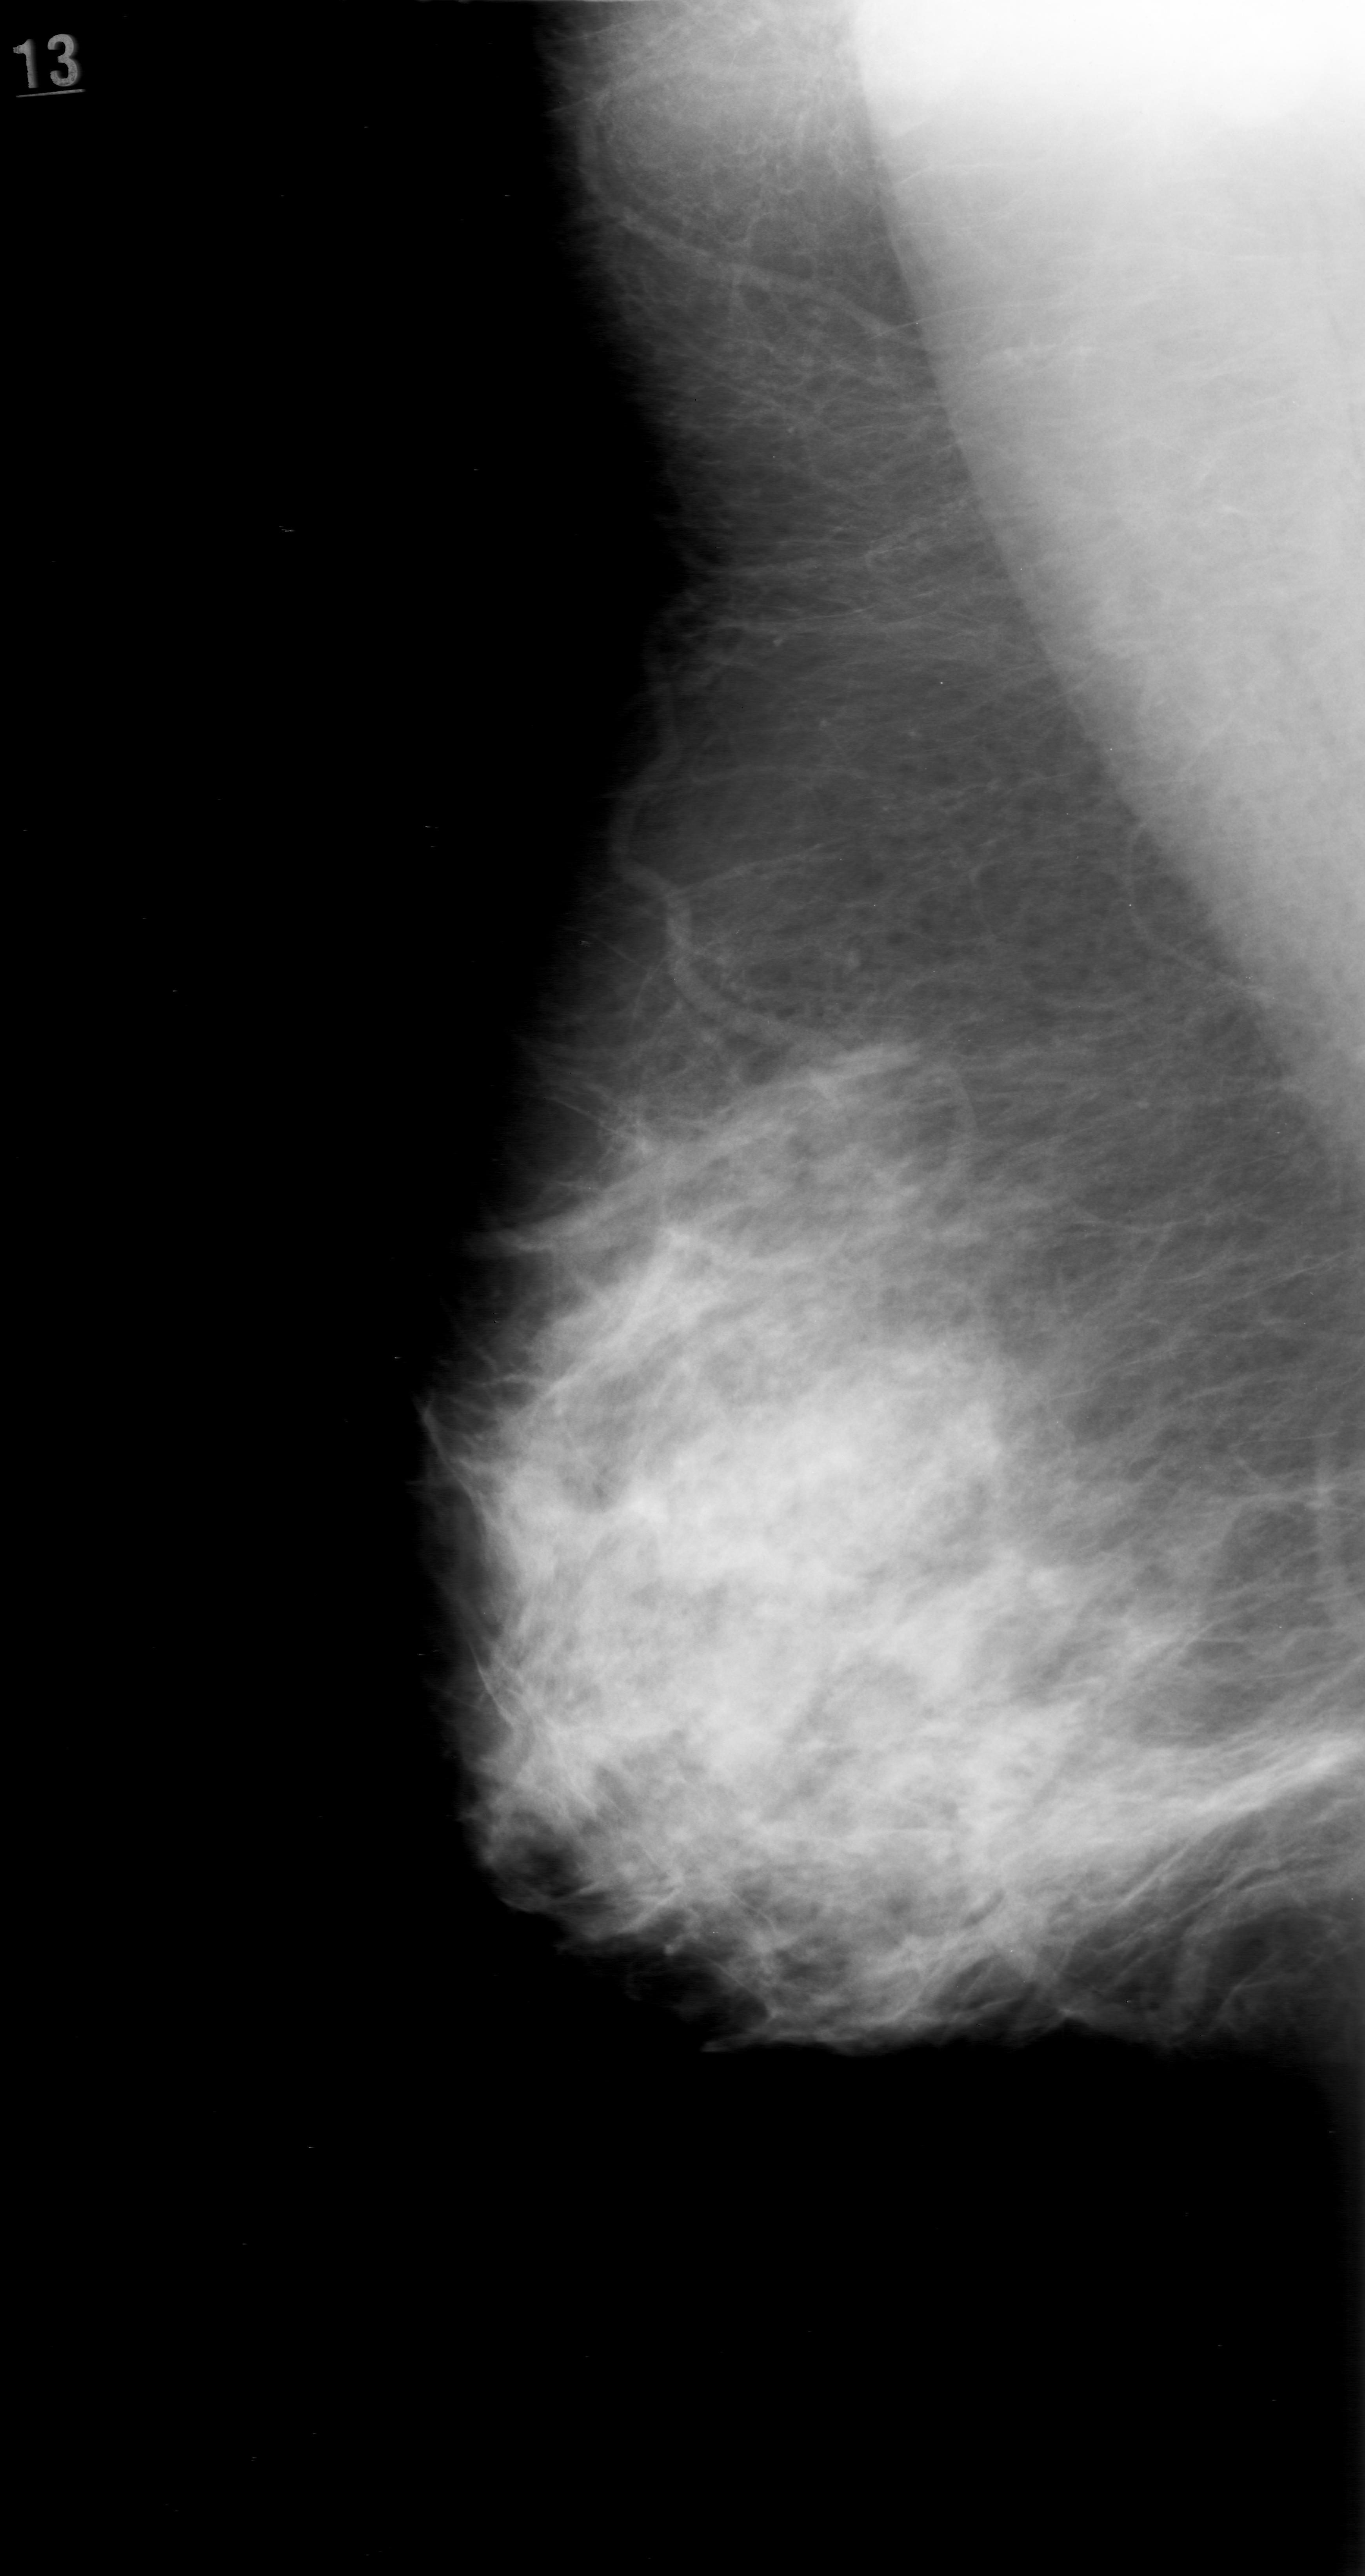
Mammogram (digitized film), right breast, mediolateral oblique (MLO) view, BI-RADS breast density category 3 (scale 1–4).
- Radiologist-marked abnormalities on this image: calcifications, morphology punctate, distribution clustered; BI-RADS assessment category 0 (incomplete: needs additional imaging); pathology (as recorded): benign.